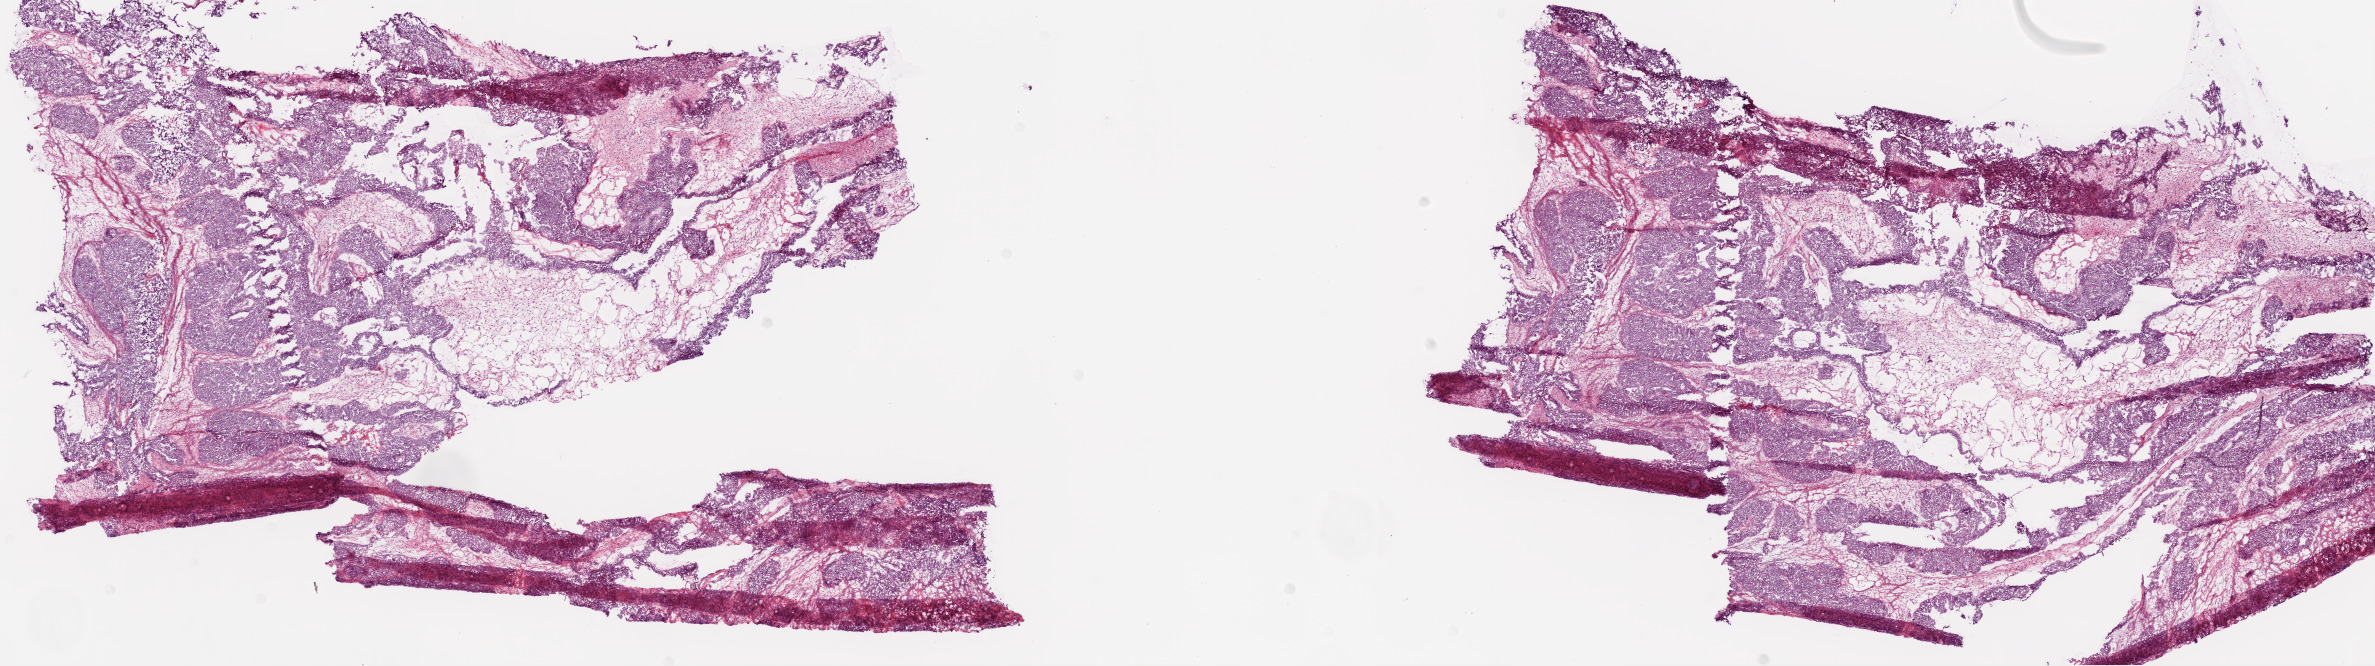
Digitized Hematoxylin and eosin (H&E) stained tissue section (whole slide) — shown as a low-resolution overview of the whole scanned area (about 19.1 x 5.3 mm, acquisition: 20x scan), frozen section, ovary, primary tumour sample. Female patient; age at initial diagnosis 56 years. Histologic grade: G3 (poorly differentiated). Slide review estimates, as recorded: tumour cells 70%, tumour nuclei 80%, normal cells 0%, stromal cells 30%, necrosis 0%.
Histologic diagnosis: Serous cystadenocarcinoma, NOS. Laterality: bilateral. FIGO stage: IIIC.